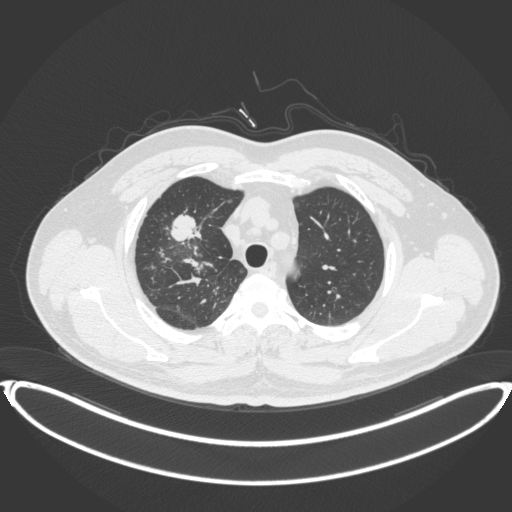
Chest CT, one axial slice; position 306 of 399 along the scan axis; 120 kVp; lung window (W 1500 / L -600 HU); 512 × 512 image matrix, field of view 445 × 445 mm. Patient: male, 53 years. From the clinical record (not read from this slice): clinical TNM (as recorded): T2a N0 M0.
Outlined on this slice (bounding box drawn by a radiologist):
- lung tumour (recorded histology: adenocarcinoma): bounding box <168,209,208,246> (left, top, right, bottom; pixels)